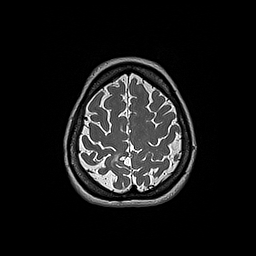
Brain MRI from a brain-tumour surgery series, one axial slice; position 50 of 192 along the scan axis; 1 mm slice thickness; 256 × 256 image matrix, field of view 250 × 250 mm. From the clinical record (not read from this slice): histopathology: Oligodendroglioma; WHO grade: 2; IDH mutation: yes.
Annotated regions visible in this slice (manually delineated by an expert):
- tumour: bounding box [x1, y1, x2, y2] px = [112, 154, 119, 163]